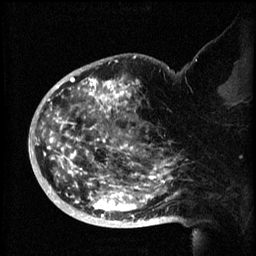
Breast MRI (dynamic contrast-enhanced), one sagittal slice; slice 40 of 60 in the series (ordered by position); 3 images stored at this slice position (order not interpretable as contrast timing); 1.5 T; TE 4.2 ms, TR 8.2 ms; 2 mm slice thickness; 256 × 256 image matrix, field of view 200 × 200 mm. Patient: female, 50 years.
Structures marked on this image (semi-automatic segmentation, software-assisted and operator-edited):
- analysis volume of interest (the breast-tissue region the enhancement analysis was run in; not a lesion): bounding box <44,72,173,219> (left, top, right, bottom; pixels)
- tumour enhancement mask (voxels above the 70 % enhancement threshold inside the analysis volume of interest): <44,74,172,219>